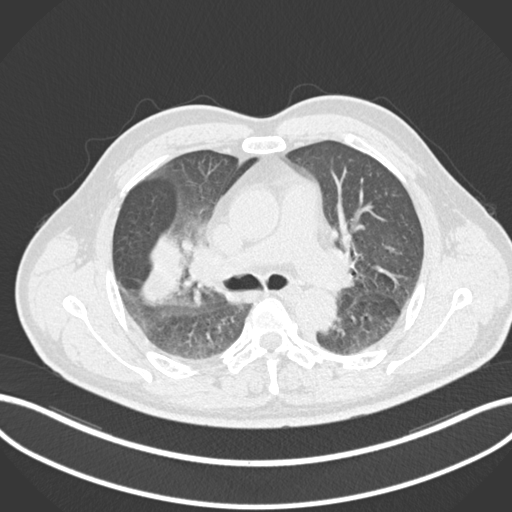
Chest CT, one axial slice; slice 643 of 852 in the series (ordered by position); reconstruction kernel B30f; lung window (W 1500 / L -600 HU); 512 × 512 image matrix. Male patient, age 55 years. From the clinical record (not read from this slice): clinical TNM (as recorded): T3 N2 M1.
Structures marked on this image (rectangle marked by the reading radiologist):
- lung tumour (recorded histology: adenocarcinoma): bounding box [x1, y1, x2, y2] px = [137, 230, 184, 309]